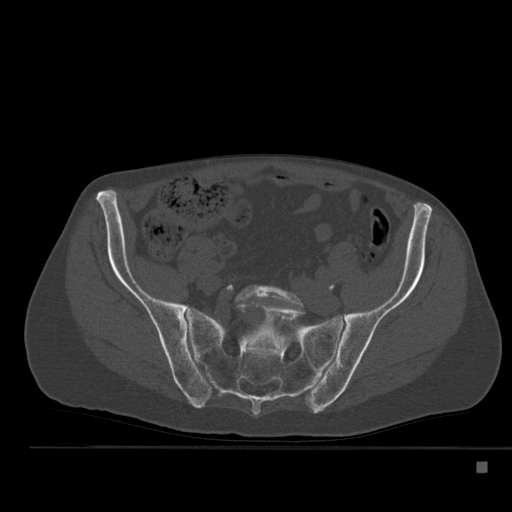
CT including the spine, one axial slice; slice 98 of 517 in the series (ordered by position); bone window (W 1800 / L 400 HU); 512 × 512 image matrix, field of view 408 × 408 mm. Male patient, age 70 years. From the clinical record (not read from this slice): primary cancer: renal.
Structures marked on this image (semi-automatic segmentation, software-assisted and operator-edited):
- L5 vertebra: box from (x=235, y=284) to (x=305, y=308) px